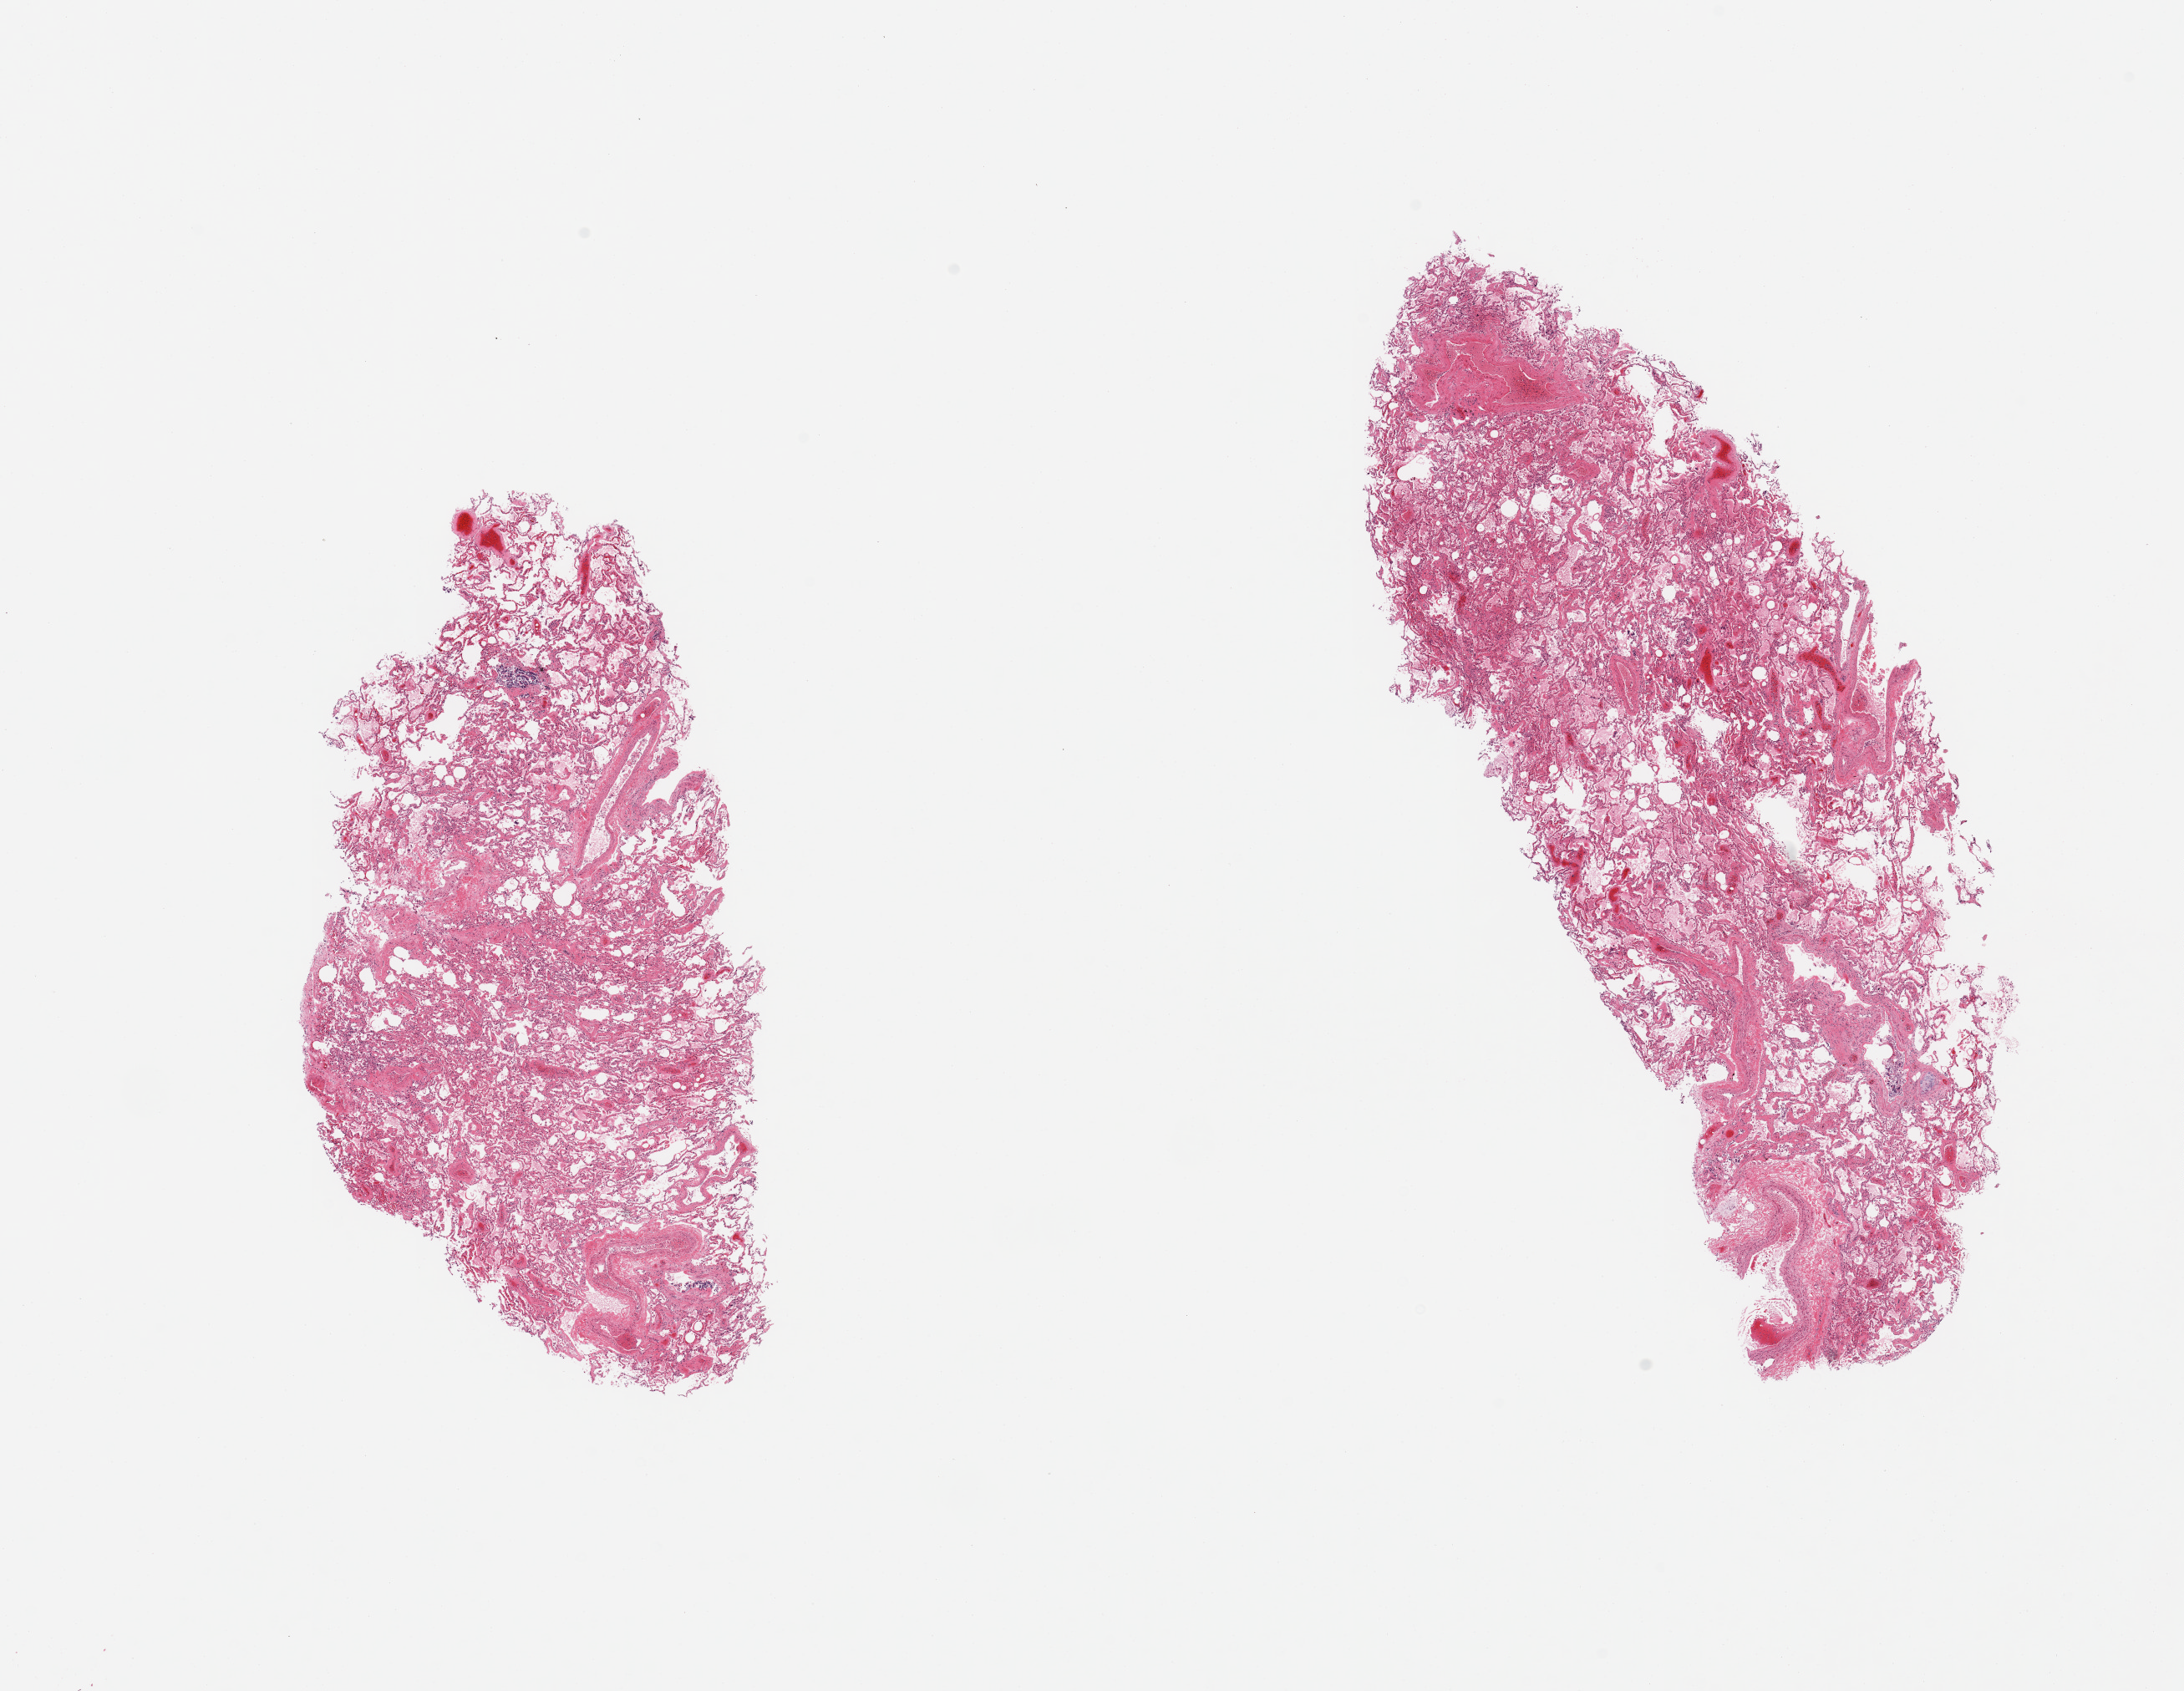
H&E whole-slide image, a low-resolution overview of the entire scanned area, about 20.7 x 16.0 mm (acquisition: 20x scan); PAXgene-fixed paraffin-embedded (PFPE) section; section of lung (target tissue); tissue donor sample. Donor sex: male.
• review note (as recorded): 2 pieces, moderate congestion